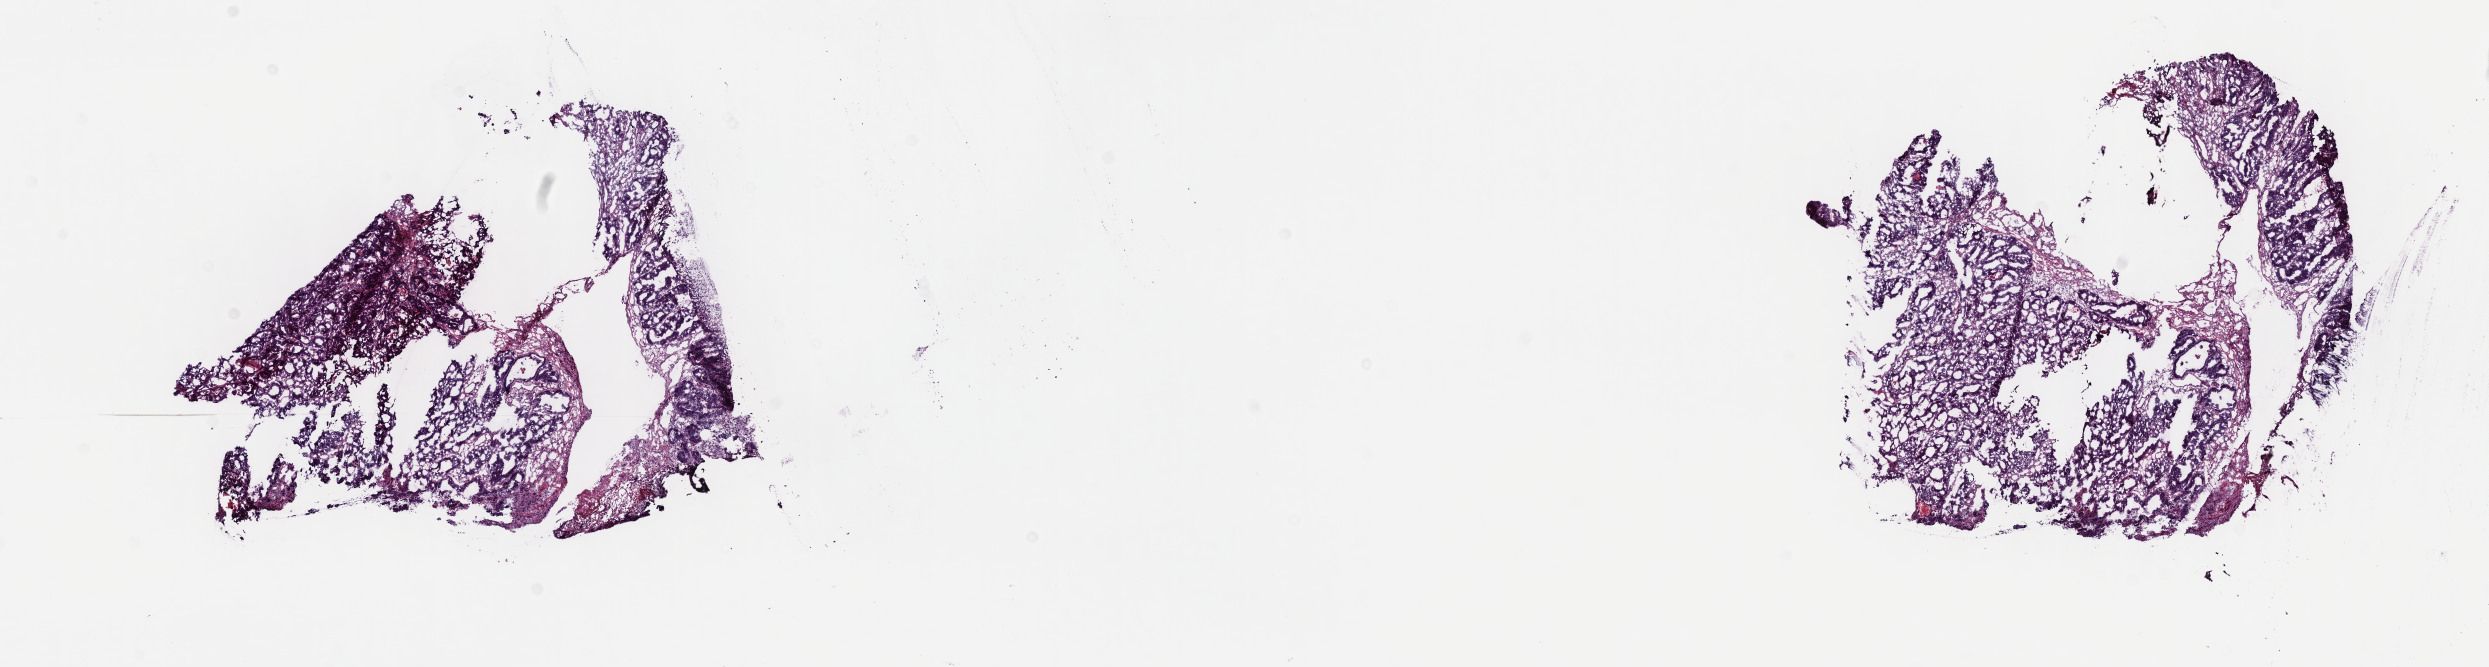
Digitized H&E tissue section (whole slide) — shown as a low-resolution overview of the whole scanned area (about 20.1 x 5.4 mm, slide scanned at 40x). Slide review estimates, as recorded: tumour cells 75%, tumour nuclei 75%, normal cells 5%, stromal cells 15%, necrosis 5%. Inflammatory infiltration, as recorded: lymphocyte infiltration 5%, monocyte infiltration 0%, neutrophil infiltration 0%.
* specimen: frozen section from the top of the tissue portion; colon, primary tumour sample